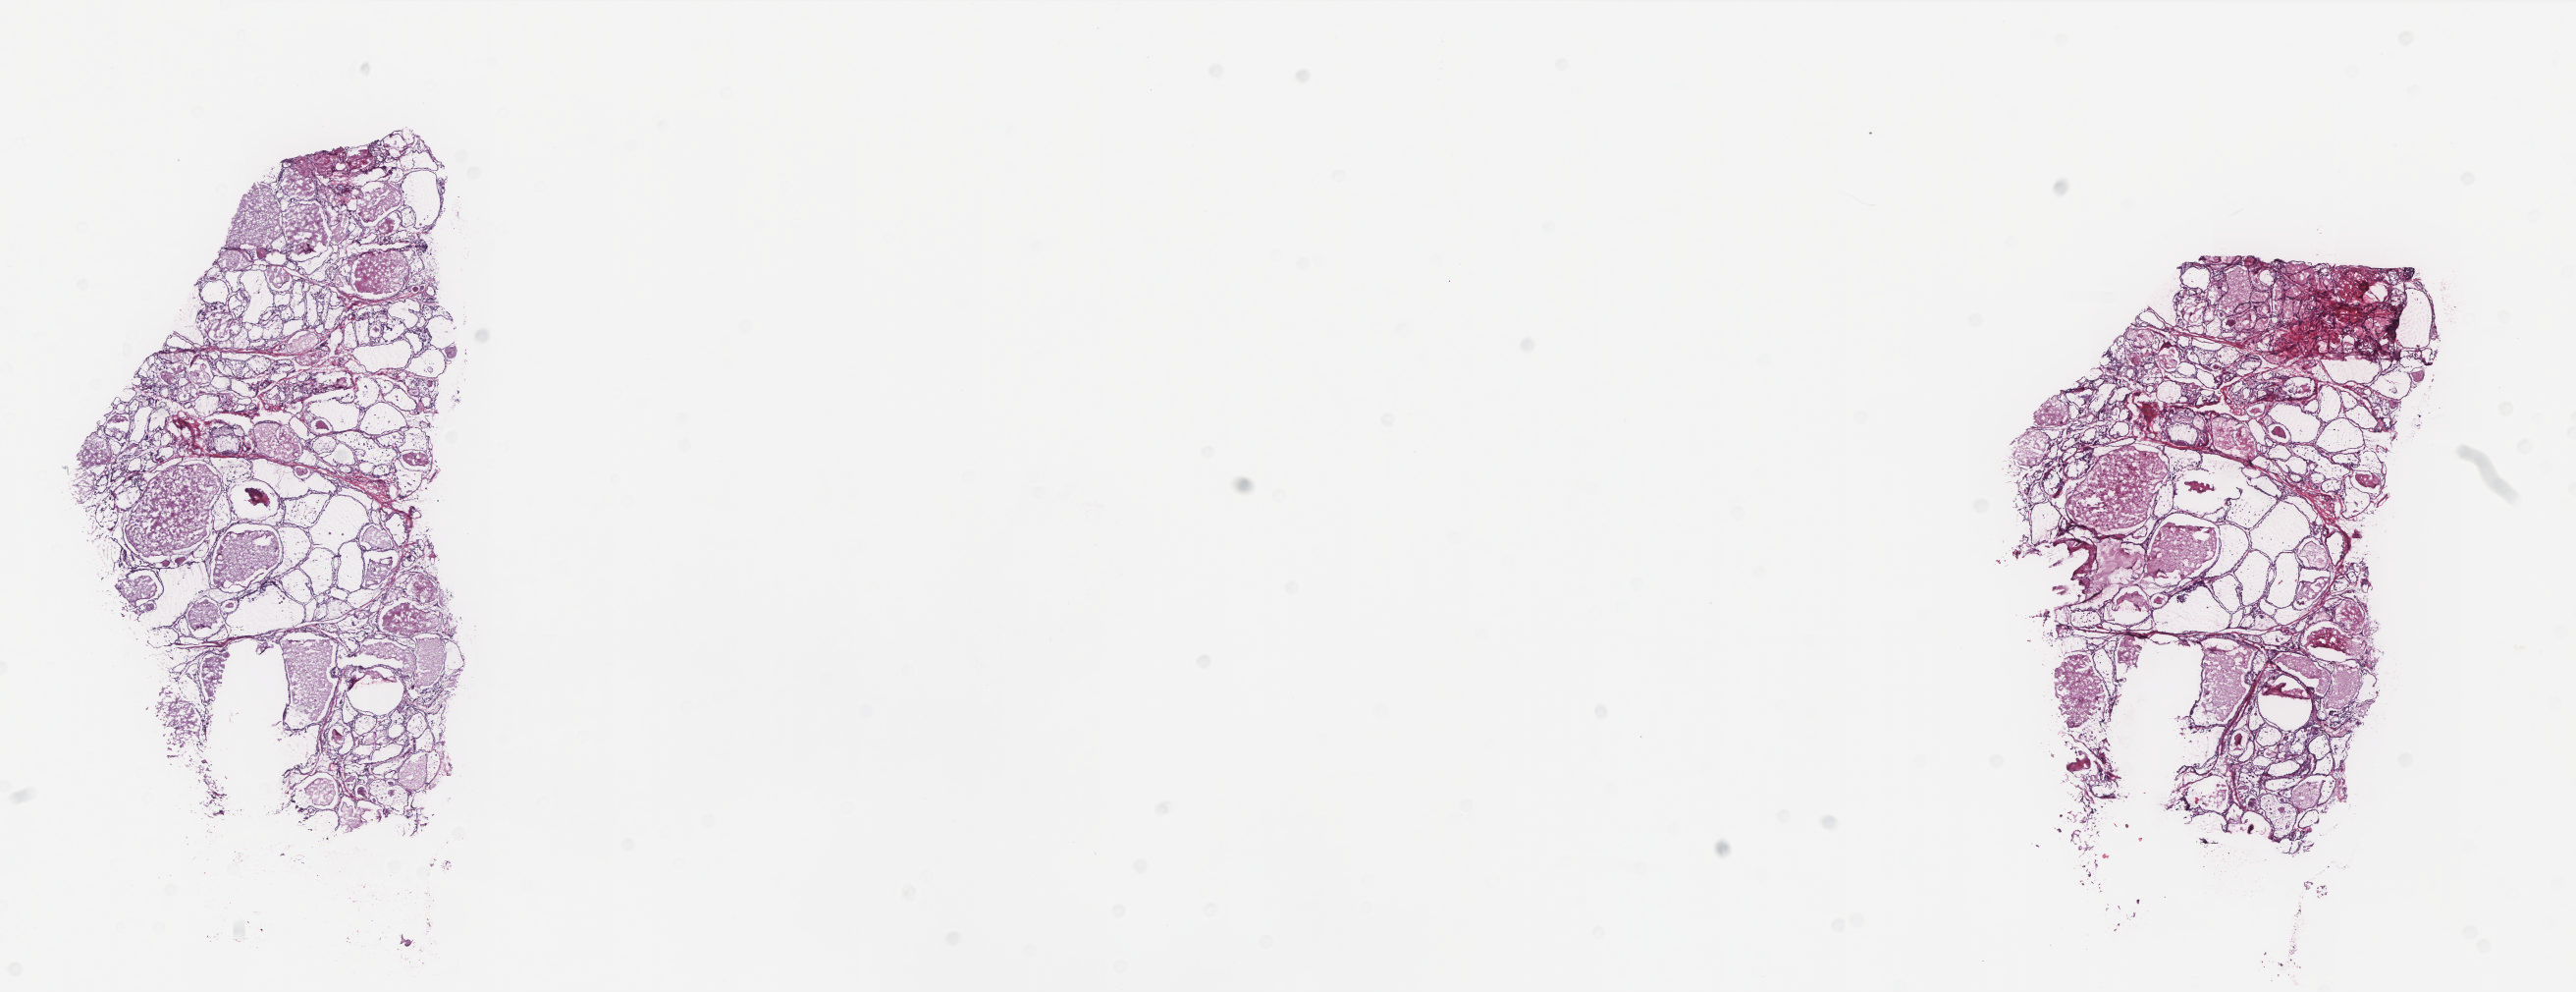
H&E-stained whole-slide image, whole scanned area (about 21.0 x 8.1 mm, slide scanned at 20x) shown as a low-resolution overview. Frozen section from the top of the tissue portion. Sample: solid tissue normal (non-tumour tissue), thyroid. Male patient; age at initial diagnosis 77 years. Slide review estimates, as recorded: tumour cells 0%, tumour nuclei 0%, normal cells 70%, stromal cells 30%, necrosis 0%. Infiltration values recorded for this section: lymphocyte infiltration 1%, monocyte infiltration 0%, neutrophil infiltration 0%.
* this section: solid tissue normal sample (biorepository sample class)
* patient diagnosis: Papillary adenocarcinoma, NOS (thyroid gland)